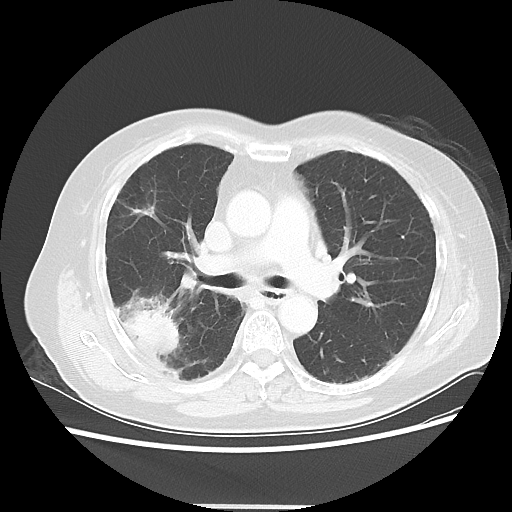
Chest CT, one axial slice; position 29 of 50 along the scan axis; reconstruction kernel LUNG; 120 kVp; lung window (W 1500 / L -600 HU); 5 mm slice thickness; 512 × 512 image matrix, field of view 360 × 360 mm. Female patient, age 72 years. From the clinical record (not read from this slice): clinical TNM (as recorded): T2 N1 M0; histopathological grade: G1.
Structures marked on this image (bounding box drawn by a radiologist):
- lung tumour (recorded histology: adenocarcinoma): bounding box (x1, y1, x2, y2) in pixels: (118, 304, 180, 355)